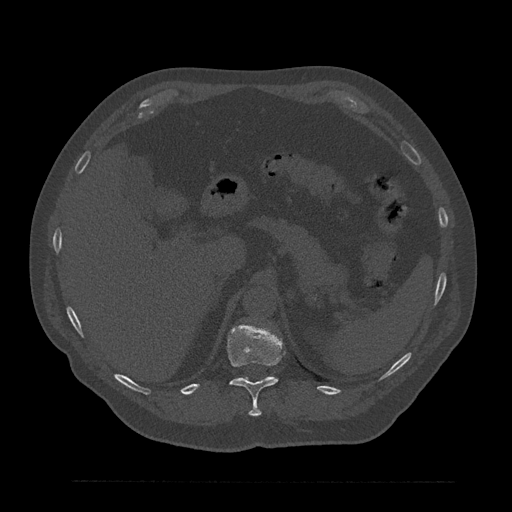
CT including the spine, one axial slice. Reconstruction kernel Br40s/3. 120 kVp. Bone window (W 1800 / L 400 HU). 0.5 mm slice thickness. 512 × 512 image matrix, field of view 430 × 430 mm. Male patient, age 61 years. From the clinical record (not read from this slice): primary cancer: prostate.
Outlined on this slice (semi-automatically segmented with operator editing):
- T11 vertebra: bounding box [x1, y1, x2, y2] px = [227, 324, 282, 416]